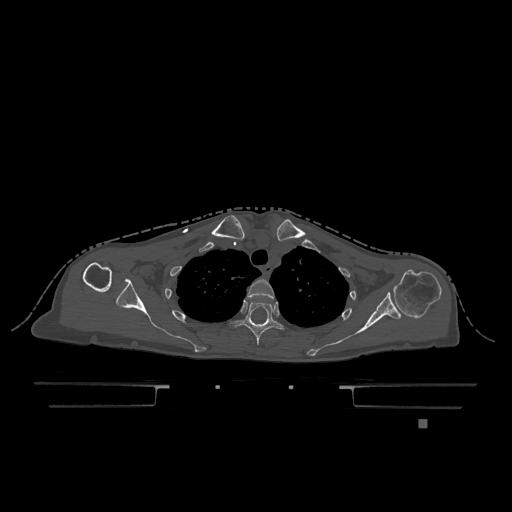
CT including the spine, one axial slice. Slice 931 of 1317 in the series (ordered by position). Bone window (W 1800 / L 400 HU). 0.5 mm slice thickness. 512 × 512 image matrix, field of view 500 × 500 mm. Female patient, age 74 years. Case-level facts recorded for this patient, not image findings: primary cancer: lung; vertebrae with lytic lesions (as recorded): T1, T4, T5, T6, L4, L5.
Structures marked on this image (semi-automatically segmented with operator editing):
- T2 vertebra: box from (x=247, y=279) to (x=275, y=299) px
- T3 vertebra: (x=230, y=302)–(x=285, y=345)